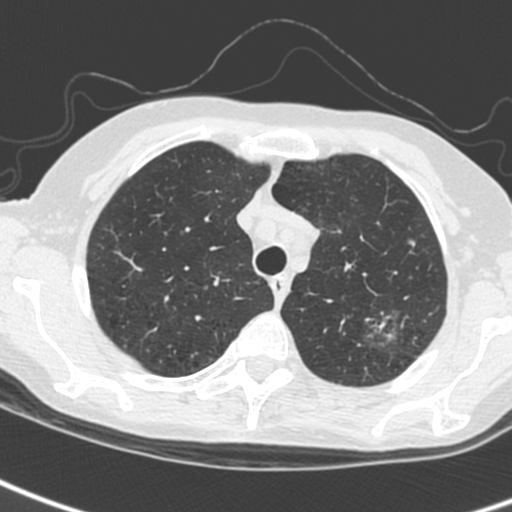
Low-dose screening chest CT, axial slice, baseline screening round, lung window (W 1500 / L -600 HU), standard (soft-tissue) reconstruction kernel (C), 120 kVp, slice 37 of 242 in the series. Female participant, aged 61 years at enrolment.
2 lesions marked by an expert reader on this slice (largest first), bounding box [x1, y1, x2, y2] px = [353, 305, 412, 352]; [395, 226, 430, 256]. The screening reader recorded 2 non-calcified nodules or masses ≥4 mm on this exam; which of them these boxes mark is not recorded. Participant outcome: lung cancer diagnosed 29 days after this screen — small cell carcinoma, NOS, left upper lobe, stage IV (AJCC 6th edition).